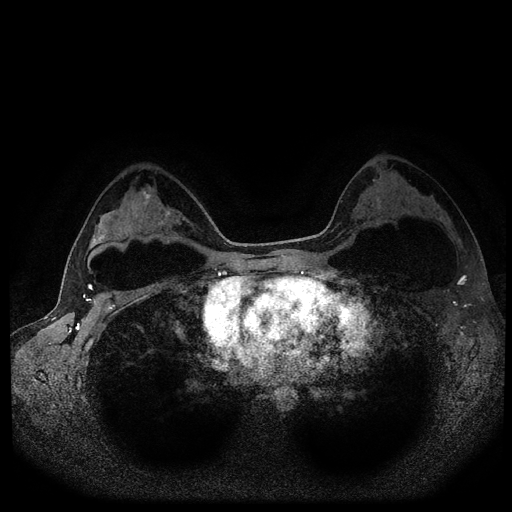
Breast MRI (dynamic contrast-enhanced, multi-phase), one axial slice; position 67 of 116 along the scan axis; dynamic contrast-enhanced series, time point 2 of 5 at this slice position (early post-contrast); 1.5 T; TE 2.6 ms, TR 5.4 ms; 2 mm slice thickness; 512 × 512 image matrix, field of view 340 × 340 mm. Female patient, age 33 years.
Outlined on this slice (semi-automatically segmented with operator editing):
- breast lesion (labelled benign in the annotation): bounding box (x1, y1, x2, y2) in pixels: (158, 209, 172, 226)
- breast lesion (labelled benign in the annotation): (141, 190, 151, 203)